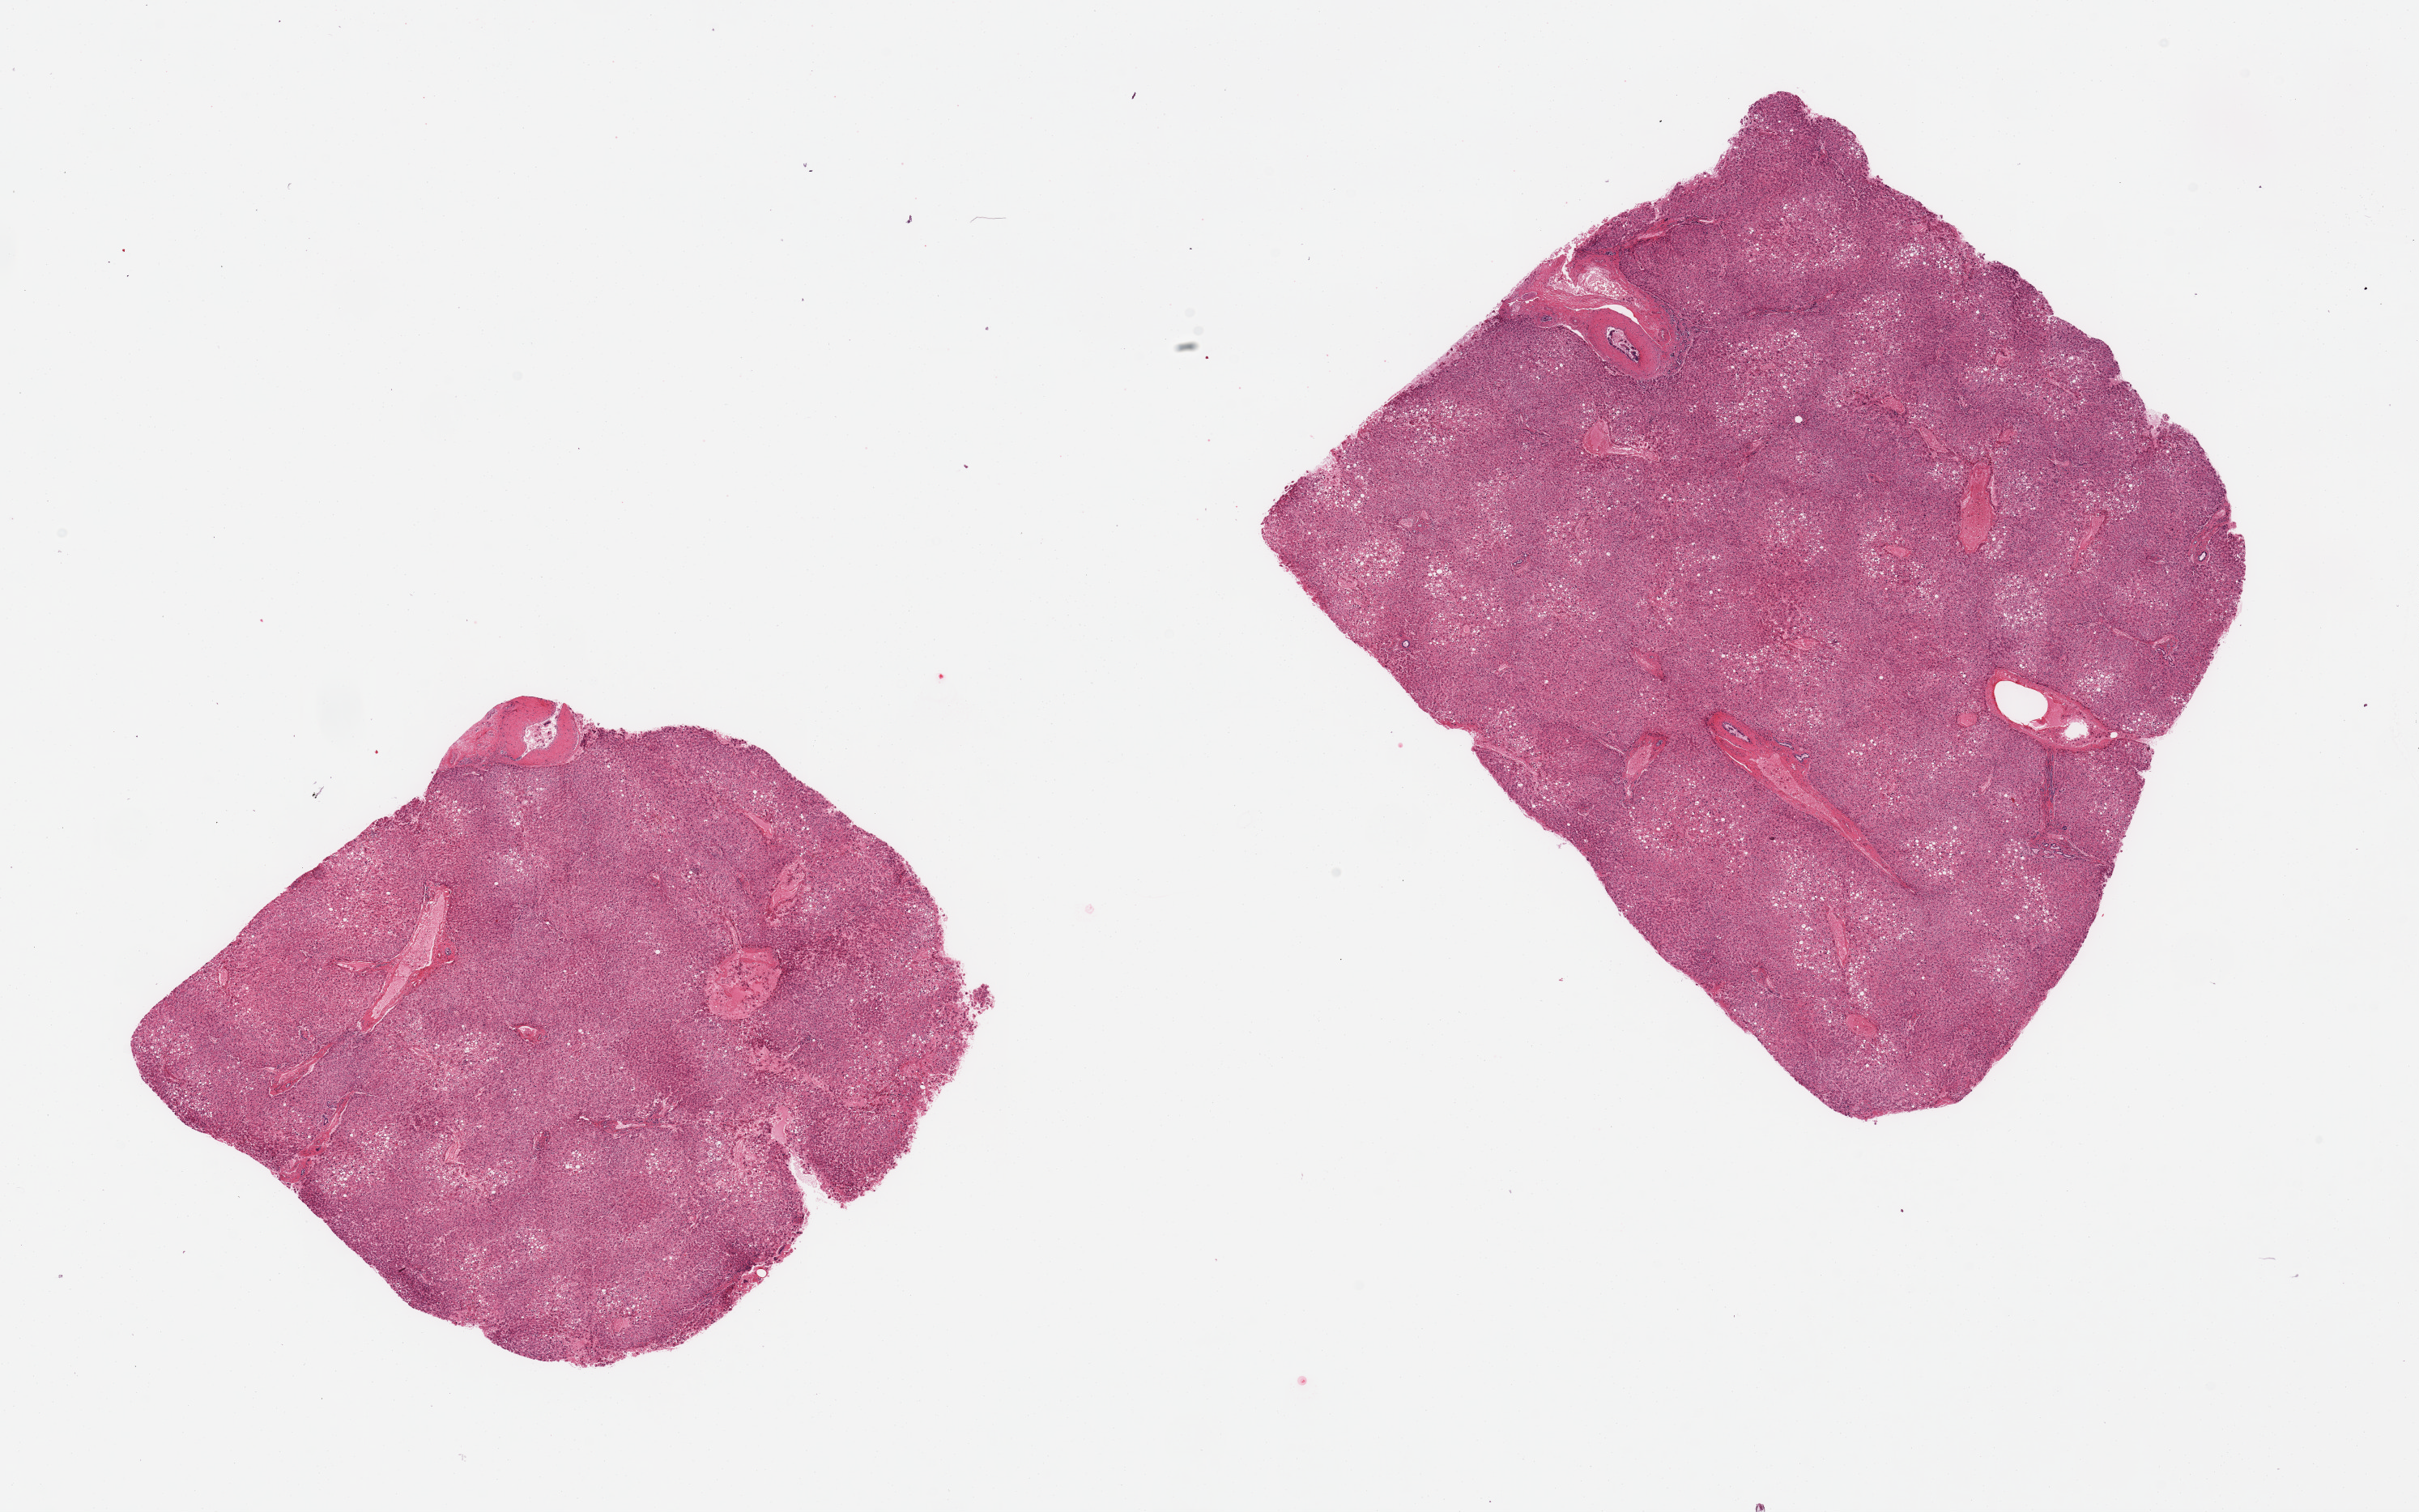
Whole-slide image, haematoxylin and eosin stain — low-resolution overview of the scanned area, about 23.6 x 14.8 mm (acquisition: 20x scan), PAXgene-fixed, paraffin-embedded tissue, sampled site (target tissue): liver, donor tissue sample. Female donor.
* reviewer comment on this tissue sample: 2 pieces; mild to moderate steatosis